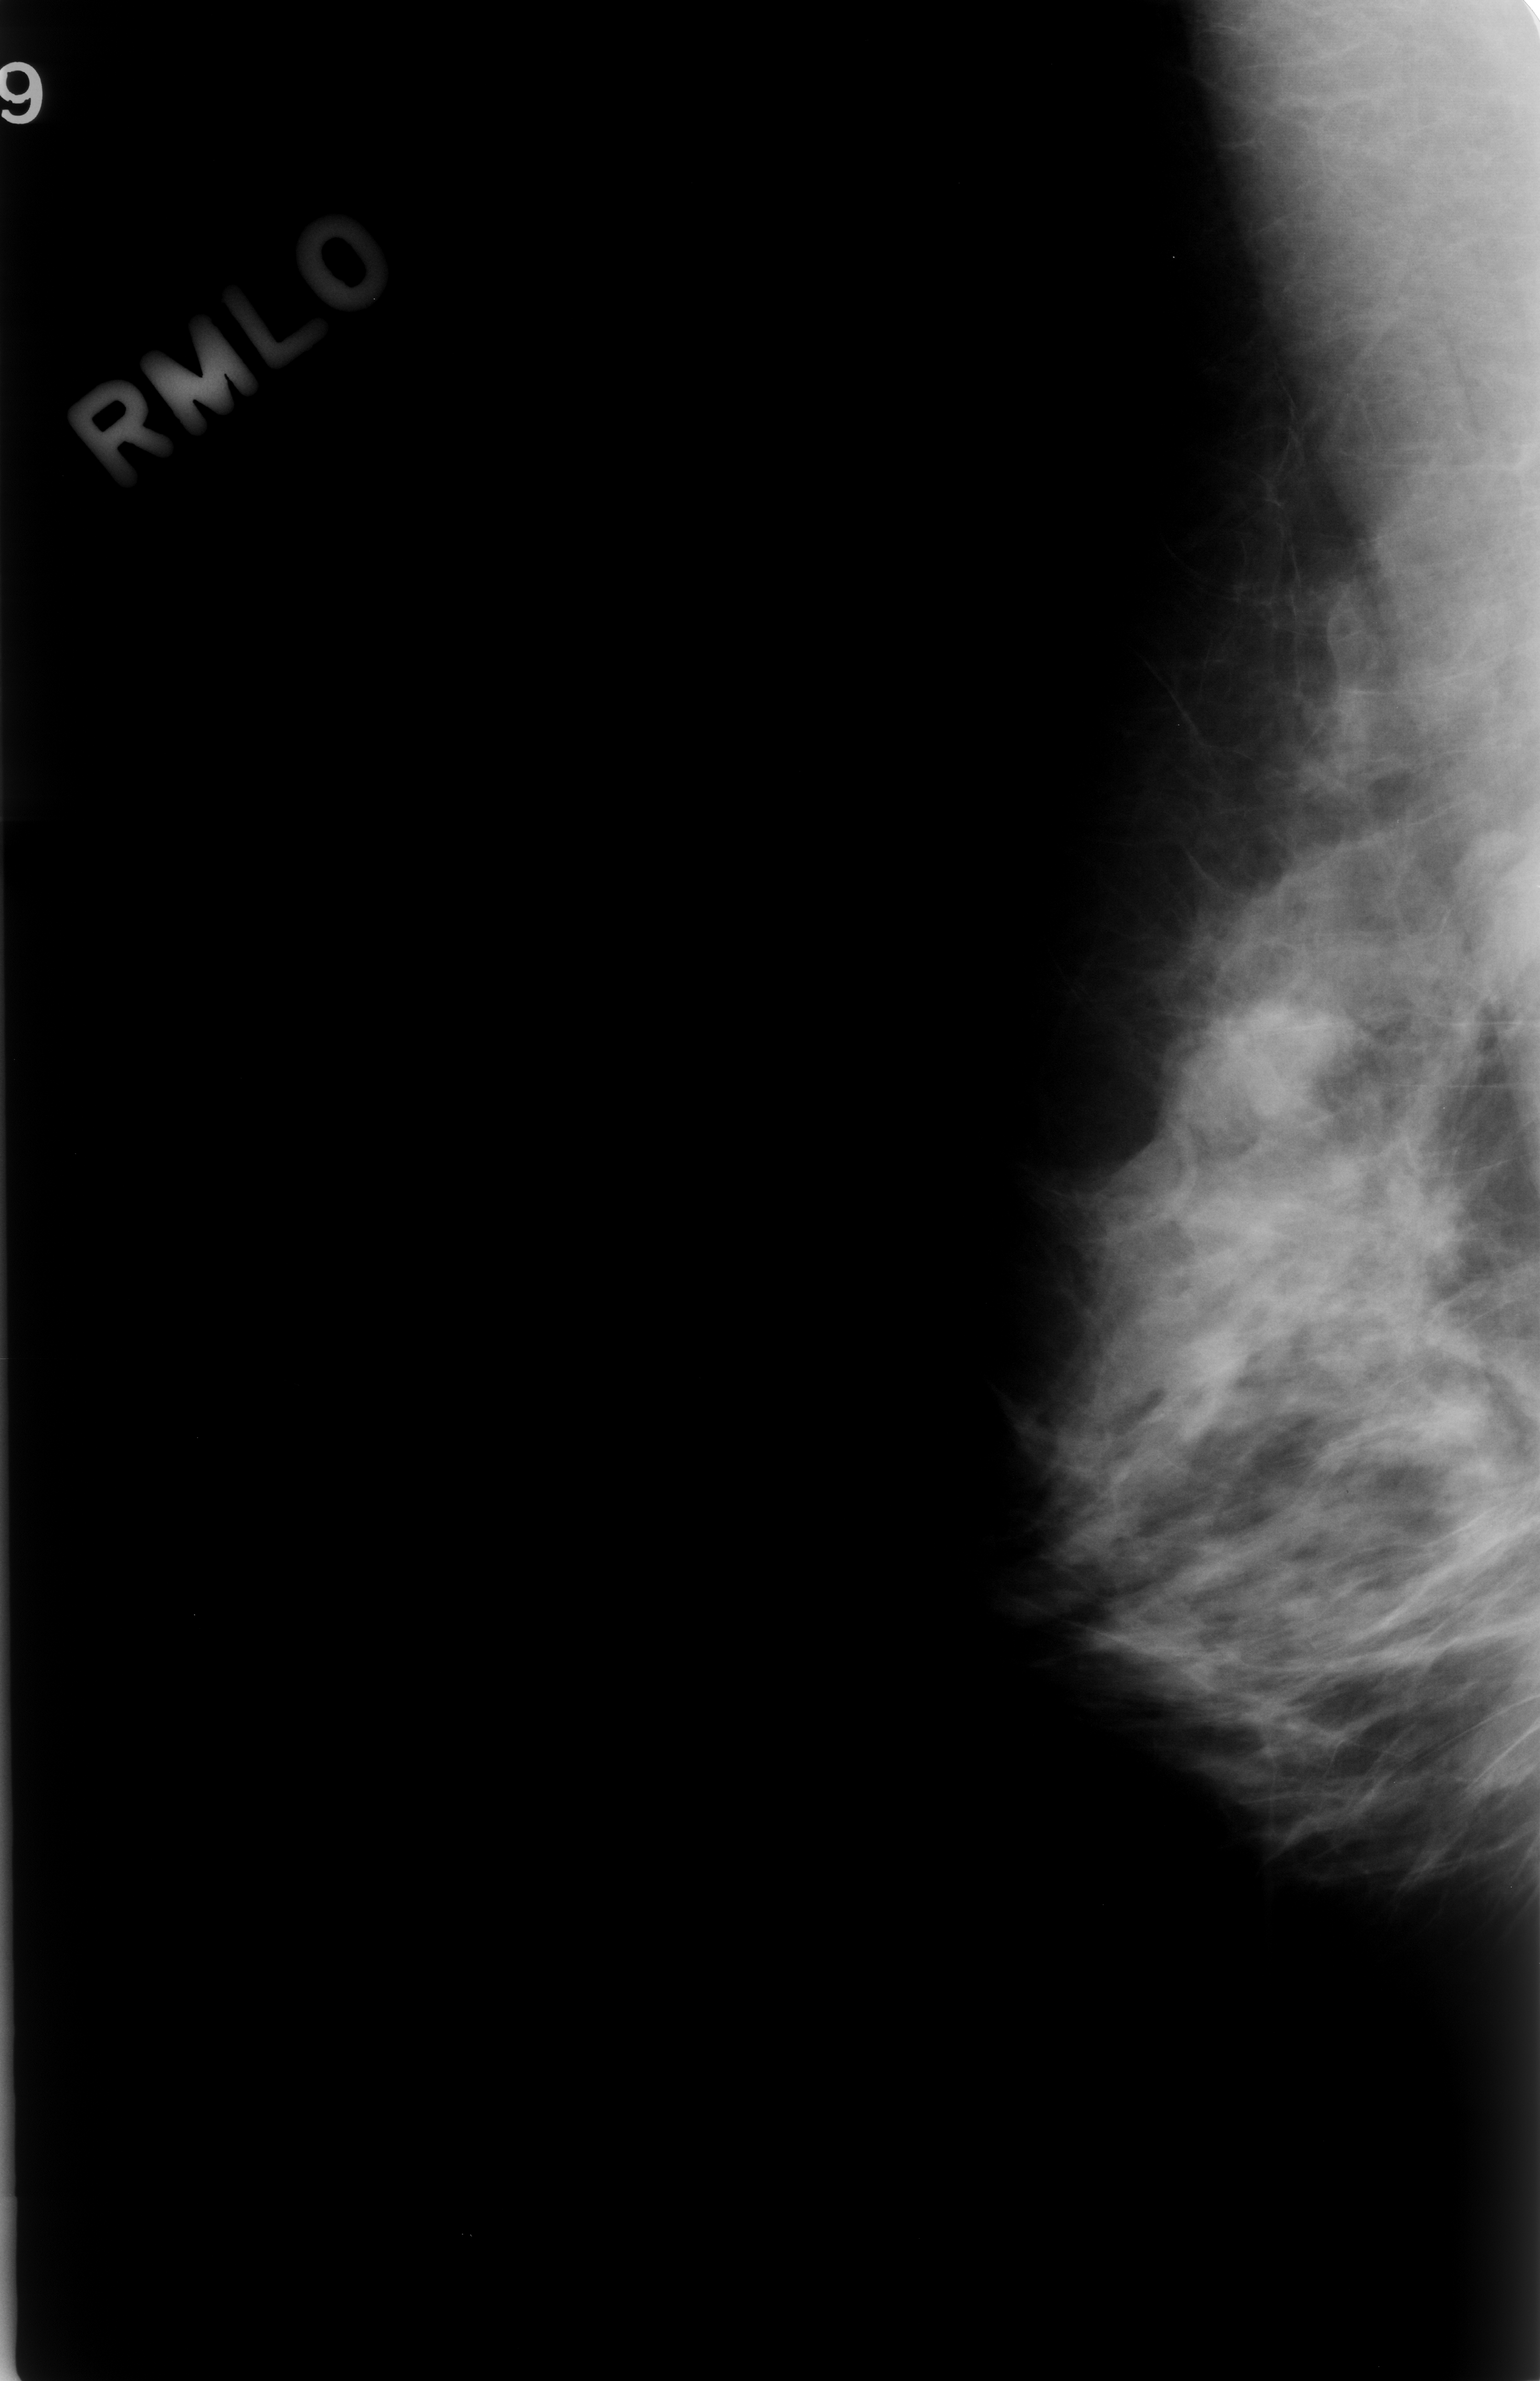
Digitized screen-film mammogram, right breast, mediolateral oblique (MLO) view, BI-RADS breast density category 3 (scale 1–4).
Abnormality record for this image: mass, shape irregular, margins spiculated; BI-RADS assessment category 4; subtlety rating 4 on a 1 (subtle) to 5 (obvious) scale; benign without callback (not worked up further).